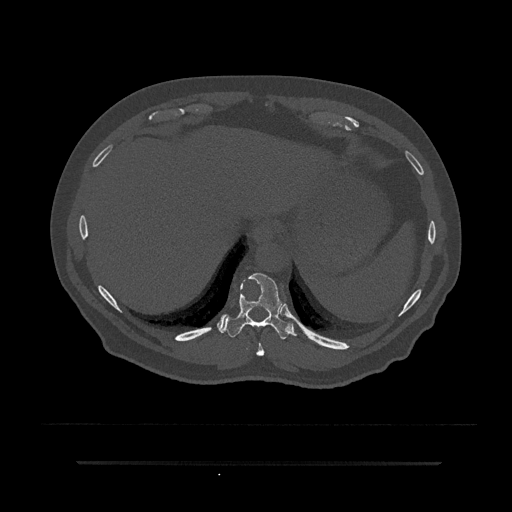
CT including the spine, one axial slice. Position 333 of 797 along the scan axis. Reconstruction kernel Br40s/3. 120 kVp. Bone window (W 1800 / L 400 HU). 0.5 mm slice thickness. 512 × 512 image matrix. Male patient, age 59 years. From the clinical record (not read from this slice): primary cancer: bile ducts.
Outlined on this slice (semi-automatically segmented with operator editing):
- T10 vertebra: bounding box [x1, y1, x2, y2] px = [223, 273, 297, 339]
- T9 vertebra: [256, 343, 265, 356]